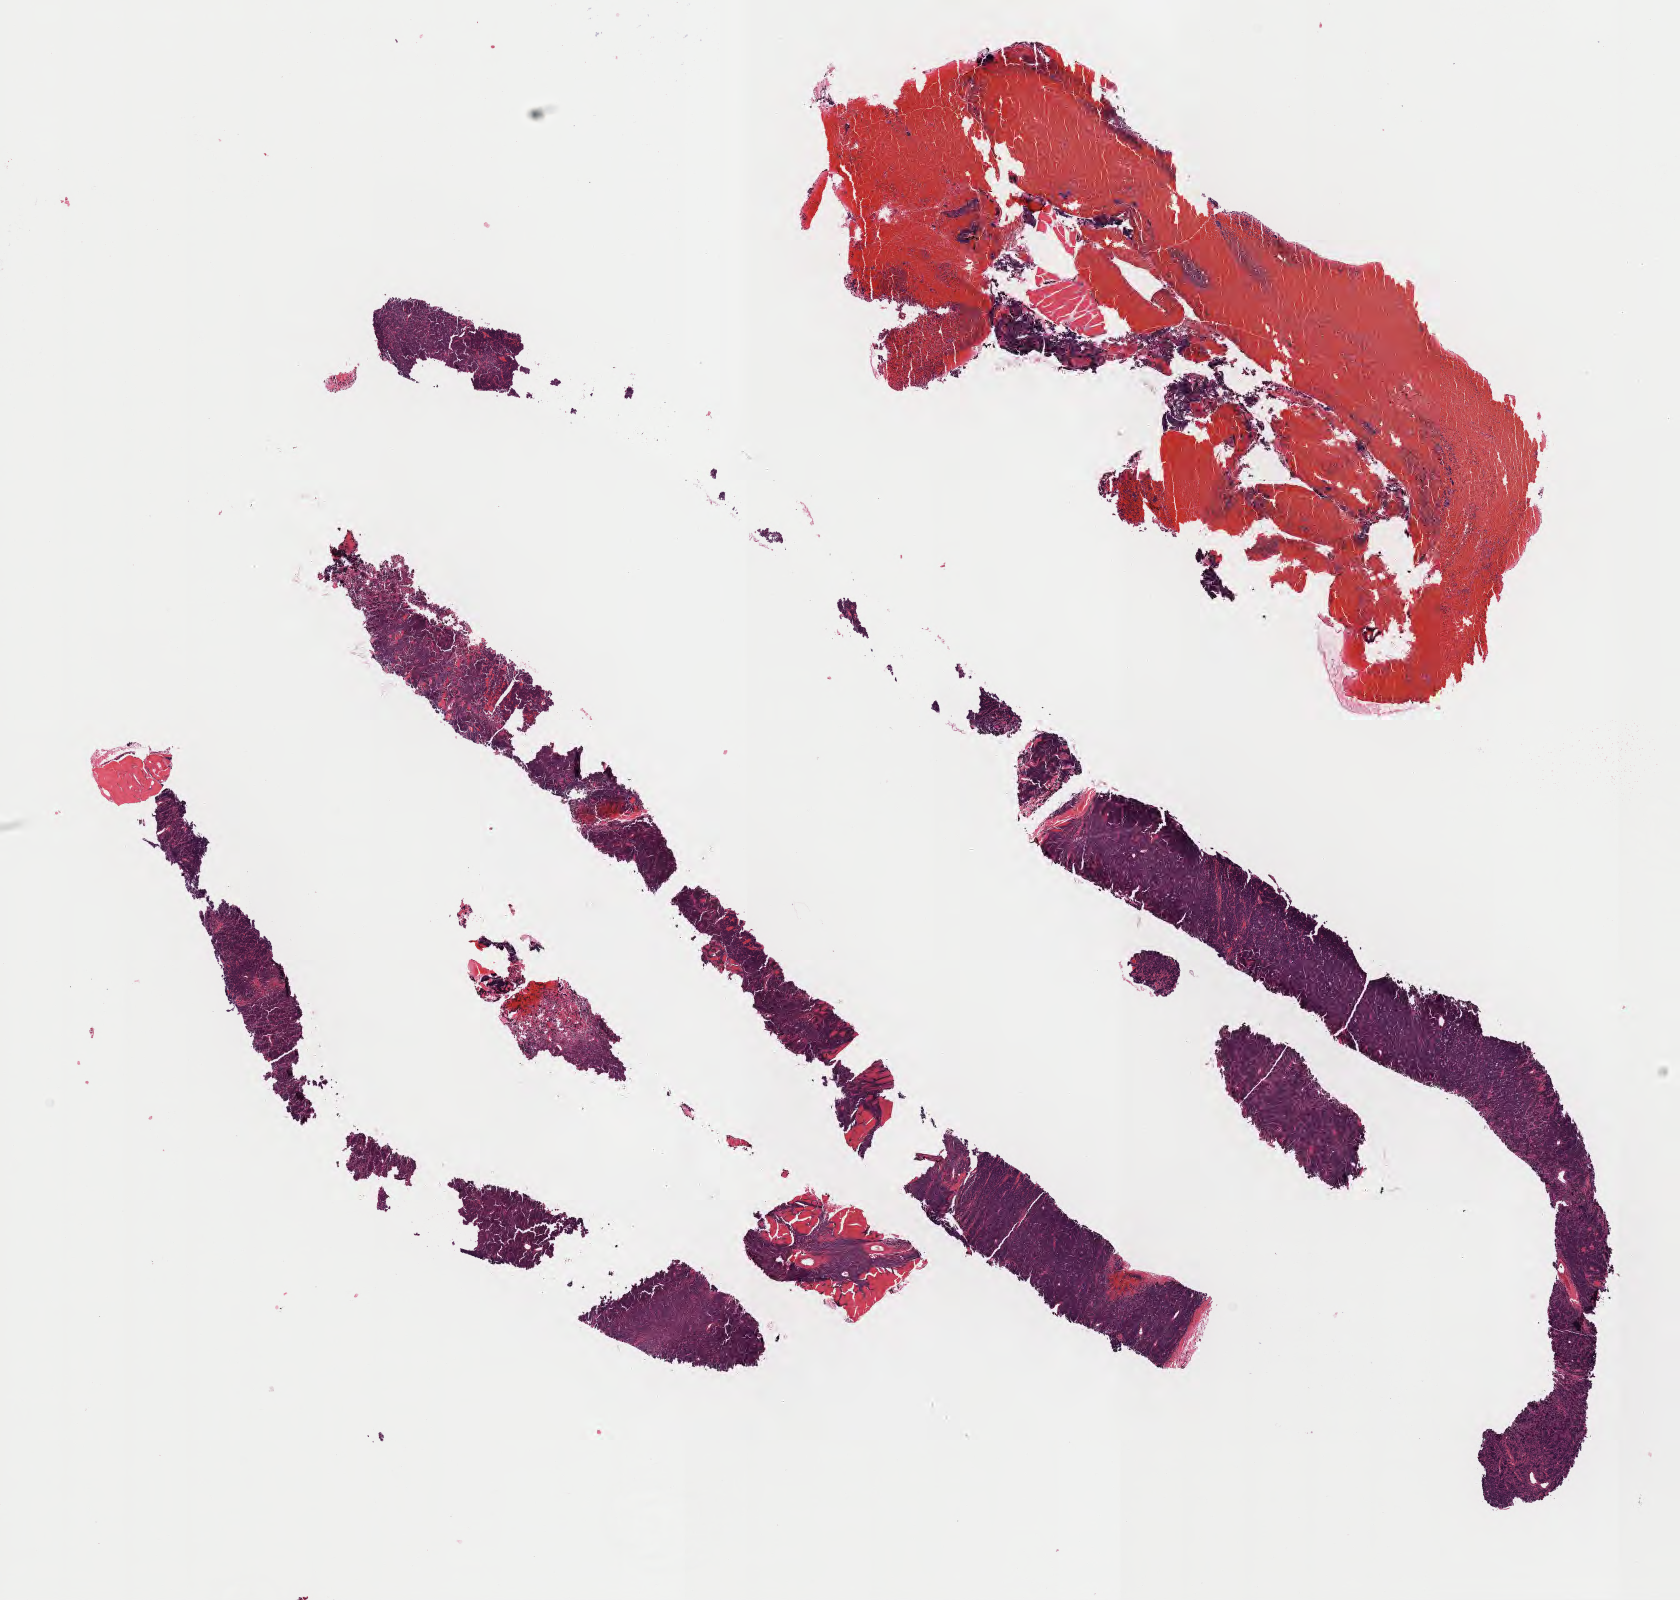
H&E whole-slide image — low-resolution overview of the scanned area, about 13.6 x 12.9 mm. Specimen: tumor tissue. Patient male; aged 29.
Histologic diagnosis: Burkitt lymphoma, NOS.